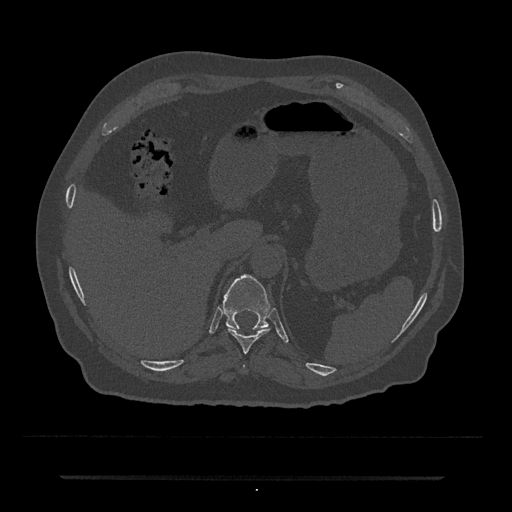
CT including the spine, one axial slice; position 206 of 797 along the scan axis; reconstruction kernel Br40s/3; 120 kVp; bone window (W 1800 / L 400 HU); 0.5 mm slice thickness; 512 × 512 image matrix, field of view 437 × 437 mm. Patient: male, 69 years. From the clinical record (not read from this slice): primary cancer: prostate.
Structures marked on this image (semi-automatically segmented with operator editing):
- T10 vertebra: bounding box <227,327,269,354> (left, top, right, bottom; pixels)
- T11 vertebra: <223,275,270,329>
- T9 vertebra: <243,365,246,368>